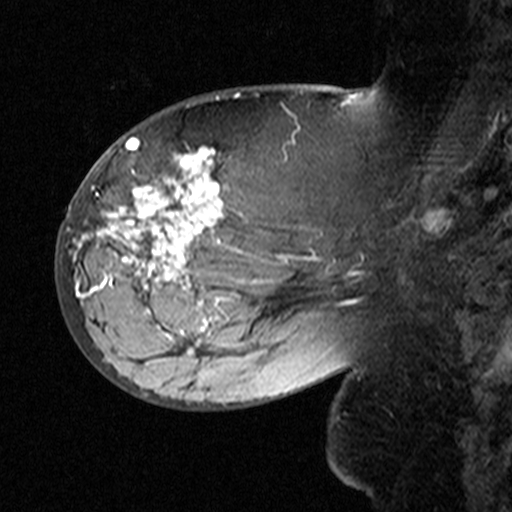
Breast MRI (dynamic contrast-enhanced), one sagittal slice. Slice 20 of 44 in the series (ordered by position). Dynamic contrast-enhanced study with each time point stored as its own series, time point 2 of 3 at this slice position (early post-contrast, ordered by acquisition time). 1.5 T. TE 4.5 ms, TR 11 ms. 512 × 512 image matrix, field of view 200 × 200 mm. Patient: female, 53 years. Case-level facts recorded for this patient, not image findings: setting: breast cancer imaged before/during neoadjuvant chemotherapy; receptor status: HR-positive, HER2-negative.
Annotated regions visible in this slice (semi-automatically segmented with operator editing):
- analysis volume of interest (the breast-tissue region the enhancement analysis was run in; not a lesion): box from (x=76, y=140) to (x=311, y=353) px
- tumour enhancement mask (voxels above the 90 % enhancement threshold inside the analysis volume of interest): (x=76, y=147)–(x=225, y=353)